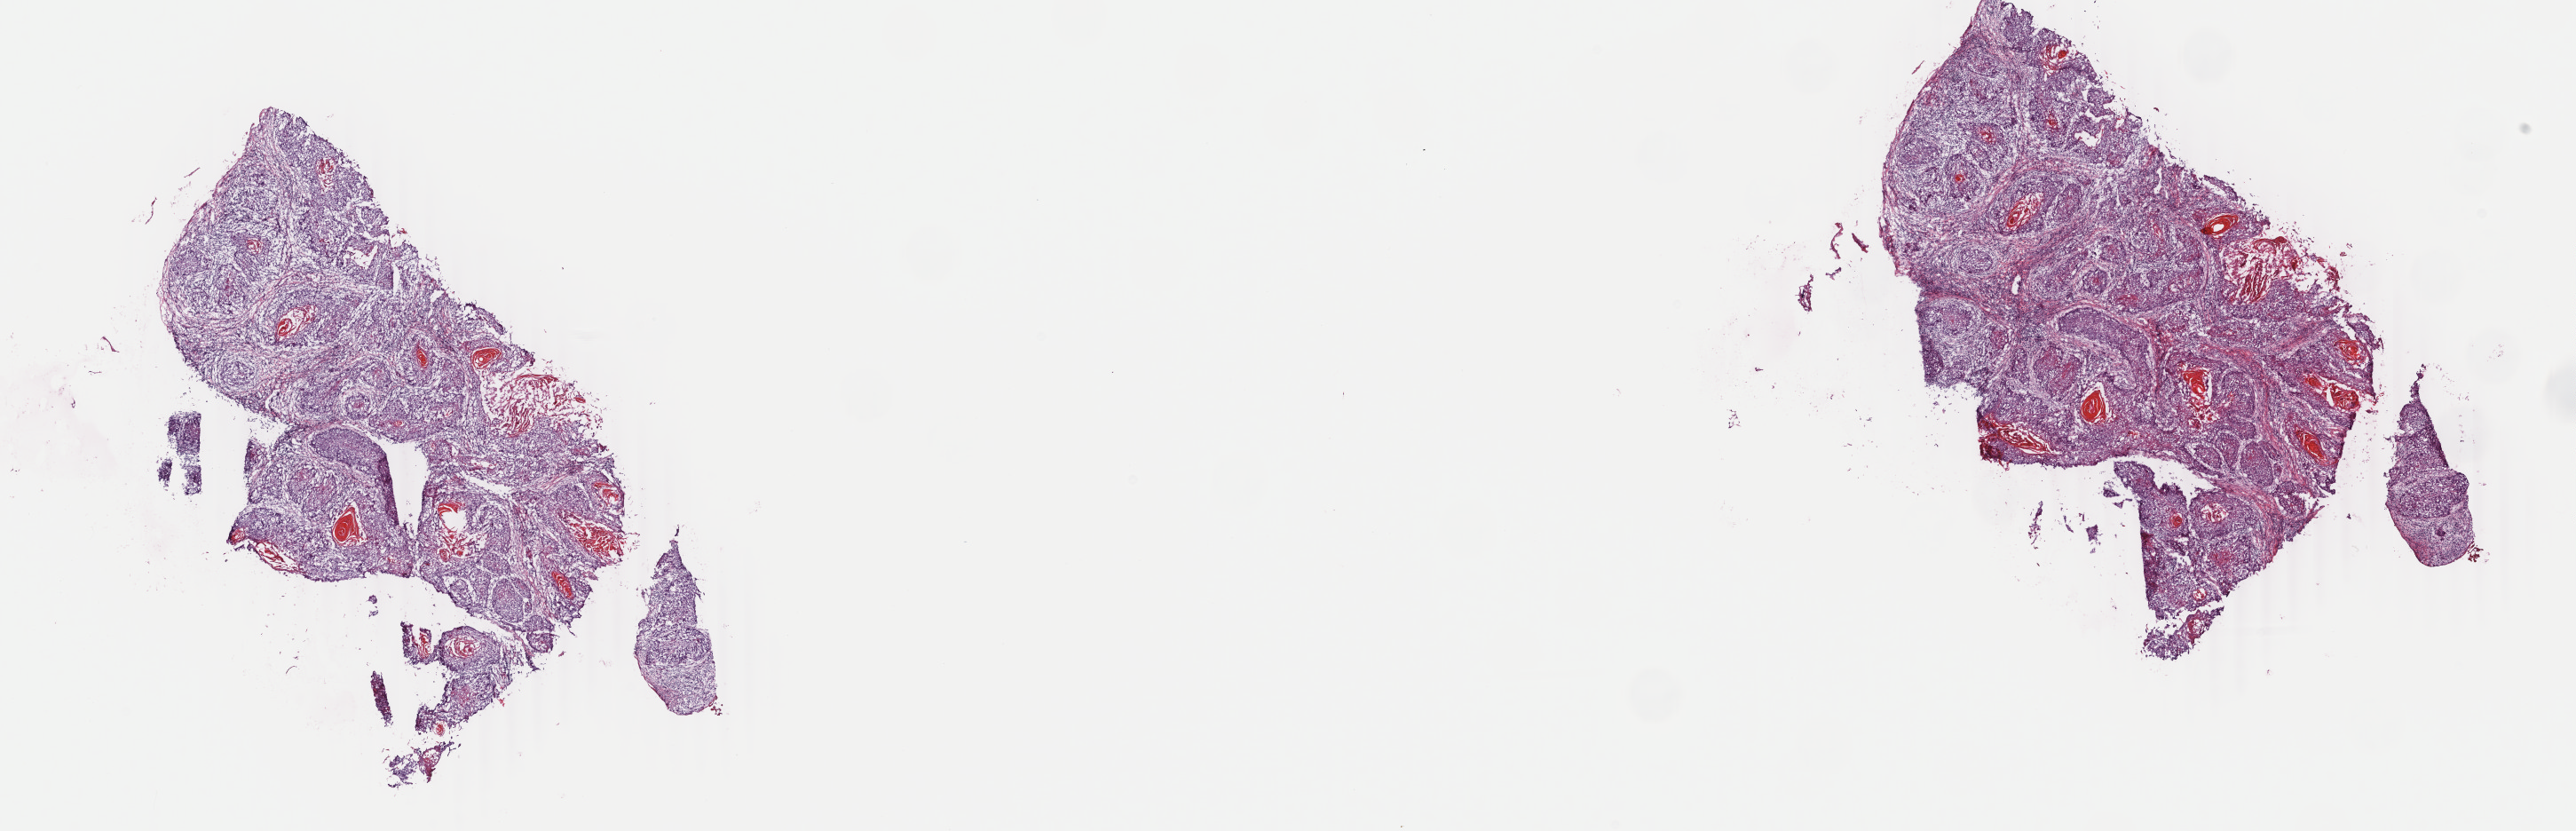
Digitized Hematoxylin and eosin (H&E) stained tissue section (whole slide), whole scanned area (about 23.1 x 7.4 mm, slide scanned at 40x) shown as a low-resolution overview; frozen section from the top of the tissue portion; primary tumour sample from the head and neck. Patient: female, age at initial diagnosis 79 years. Histologic grade: G2 (moderately differentiated). Composition of this section per pathologist review: tumour cells 55%, tumour nuclei 60%, normal cells 0%, stromal cells 40%, necrosis 5%. Inflammatory infiltration, as recorded: lymphocyte infiltration 0%, monocyte infiltration 0%, neutrophil infiltration 0%.
Lymph nodes positive (case pathology): 0 of 27 examined. Diagnosis: Squamous cell carcinoma, NOS. AJCC pathologic stage: IVA (6th edition).